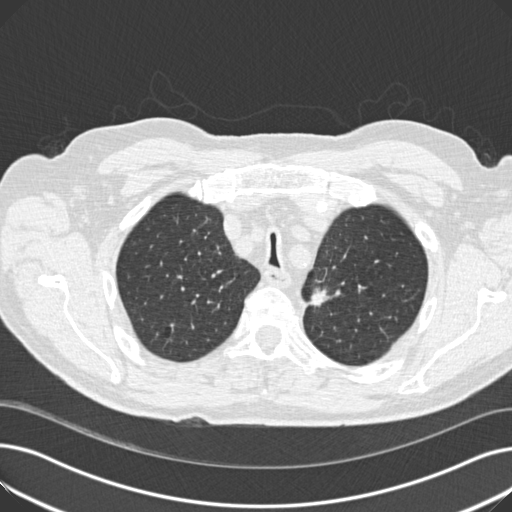
Low-dose screening chest CT, one axial slice. Slice 148 of 191 in the series (ordered by position). Reconstruction kernel B30f. Lung window (W 1500 / L -600 HU). 2 mm slice thickness. 512 × 512 image matrix, field of view 370 × 370 mm.
Structures marked on this image (outlined manually by an expert reader):
- lesion 1 (tumor, upper lobe of left lung): bounding box (x1, y1, x2, y2) in pixels: (311, 289, 329, 306)